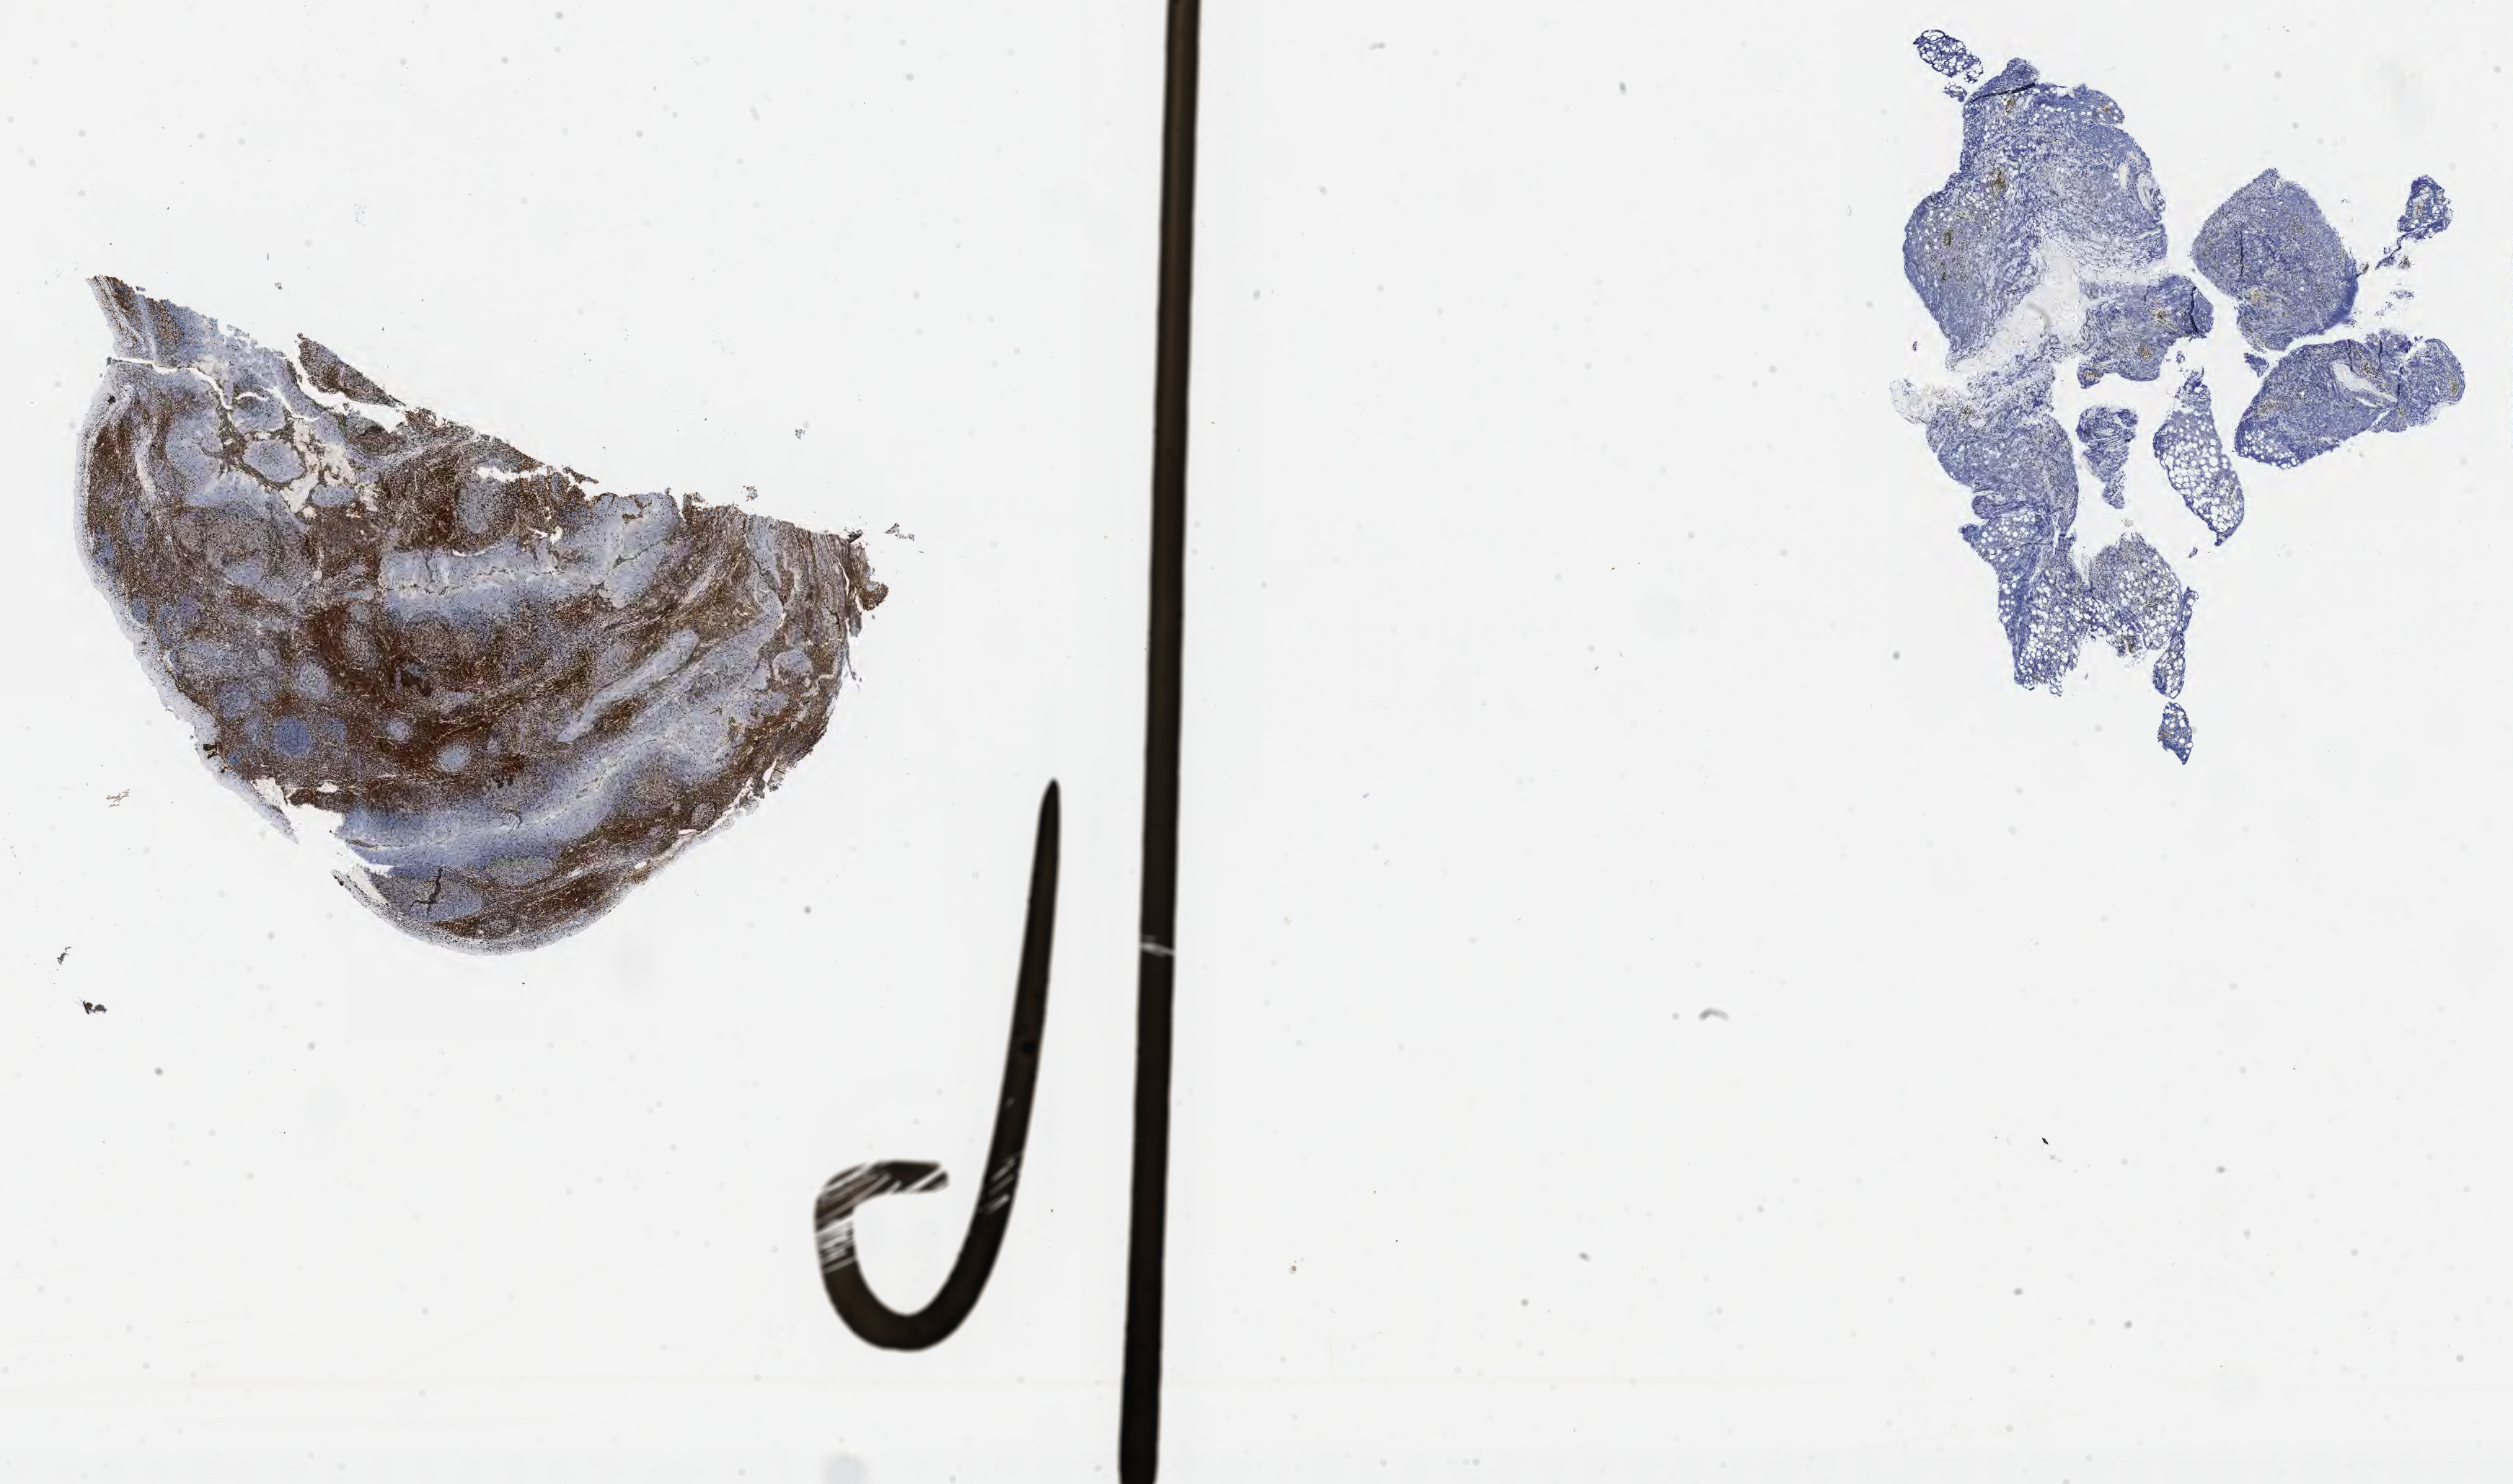
Immunohistochemistry (IHC) whole-slide image stained for CD3 — whole scanned area (about 28.2 x 16.6 mm) shown as a low-resolution overview. Tumor tissue. Site: orbit. Patient: male, 20 years old.
- diagnosis: Burkitt lymphoma, NOS